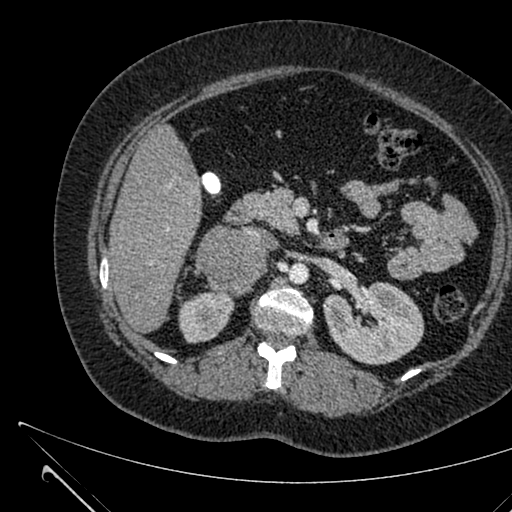
Contrast-enhanced abdominal CT, one axial slice. Position 372 of 731 along the scan axis. 120 kVp. Soft-tissue window (W 400 / L 40 HU). 512 × 512 image matrix. Patient: female, 36 years. Case-level facts recorded for this patient, not image findings: diagnosis: adrenocortical carcinoma; tumour side: right adrenal.
Annotated regions visible in this slice (semi-automatically segmented with operator editing):
- mass: bounding box (x1, y1, x2, y2) in pixels: (197, 226, 266, 294)